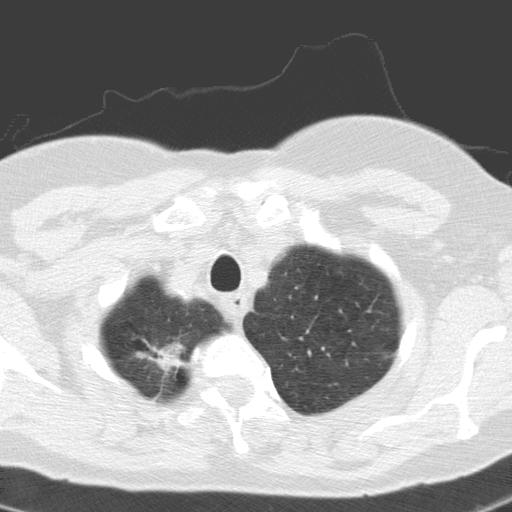
Low-dose screening chest CT, axial slice. Baseline annual screen. Lung window (W 1500 / L -600 HU). Standard (soft-tissue) reconstruction kernel (C). Slice 13 of 155 in the series. 512 × 512 image matrix, field of view 278 × 278 mm. Female, age 60 years at enrolment.
Expert-annotated lung lesion, box from (x=118, y=326) to (x=197, y=397) px. No non-calcified nodule or mass ≥4 mm was recorded by the screening reader at this exam. Later outcome: lung cancer diagnosed 391 days after this screen — squamous cell carcinoma, keratinizing, NOS, right upper lobe, moderately differentiated (G2), stage IA (AJCC 6th edition), 20 mm at pathology.